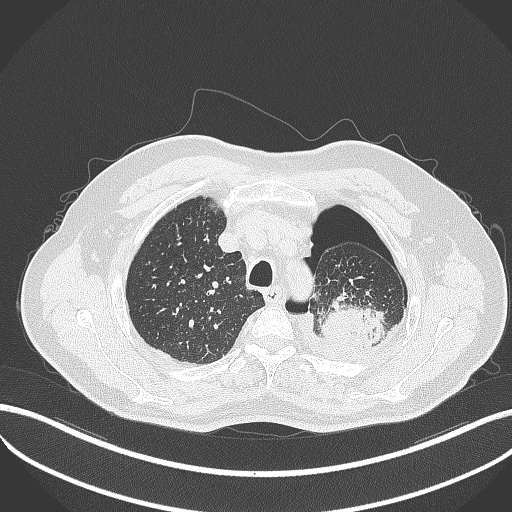
Chest CT, one axial slice; slice 408 of 464 in the series (ordered by position); 120 kVp; lung window (W 1500 / L -600 HU); 1 mm slice thickness; 512 × 512 image matrix, field of view 400 × 400 mm. Male patient, age 76 years. From the clinical record (not read from this slice): clinical TNM (as recorded): T3 N0 M1b.
Annotated regions visible in this slice (bounding box drawn by a radiologist):
- lung tumour (recorded histology: adenocarcinoma): box from (x=323, y=298) to (x=387, y=353) px